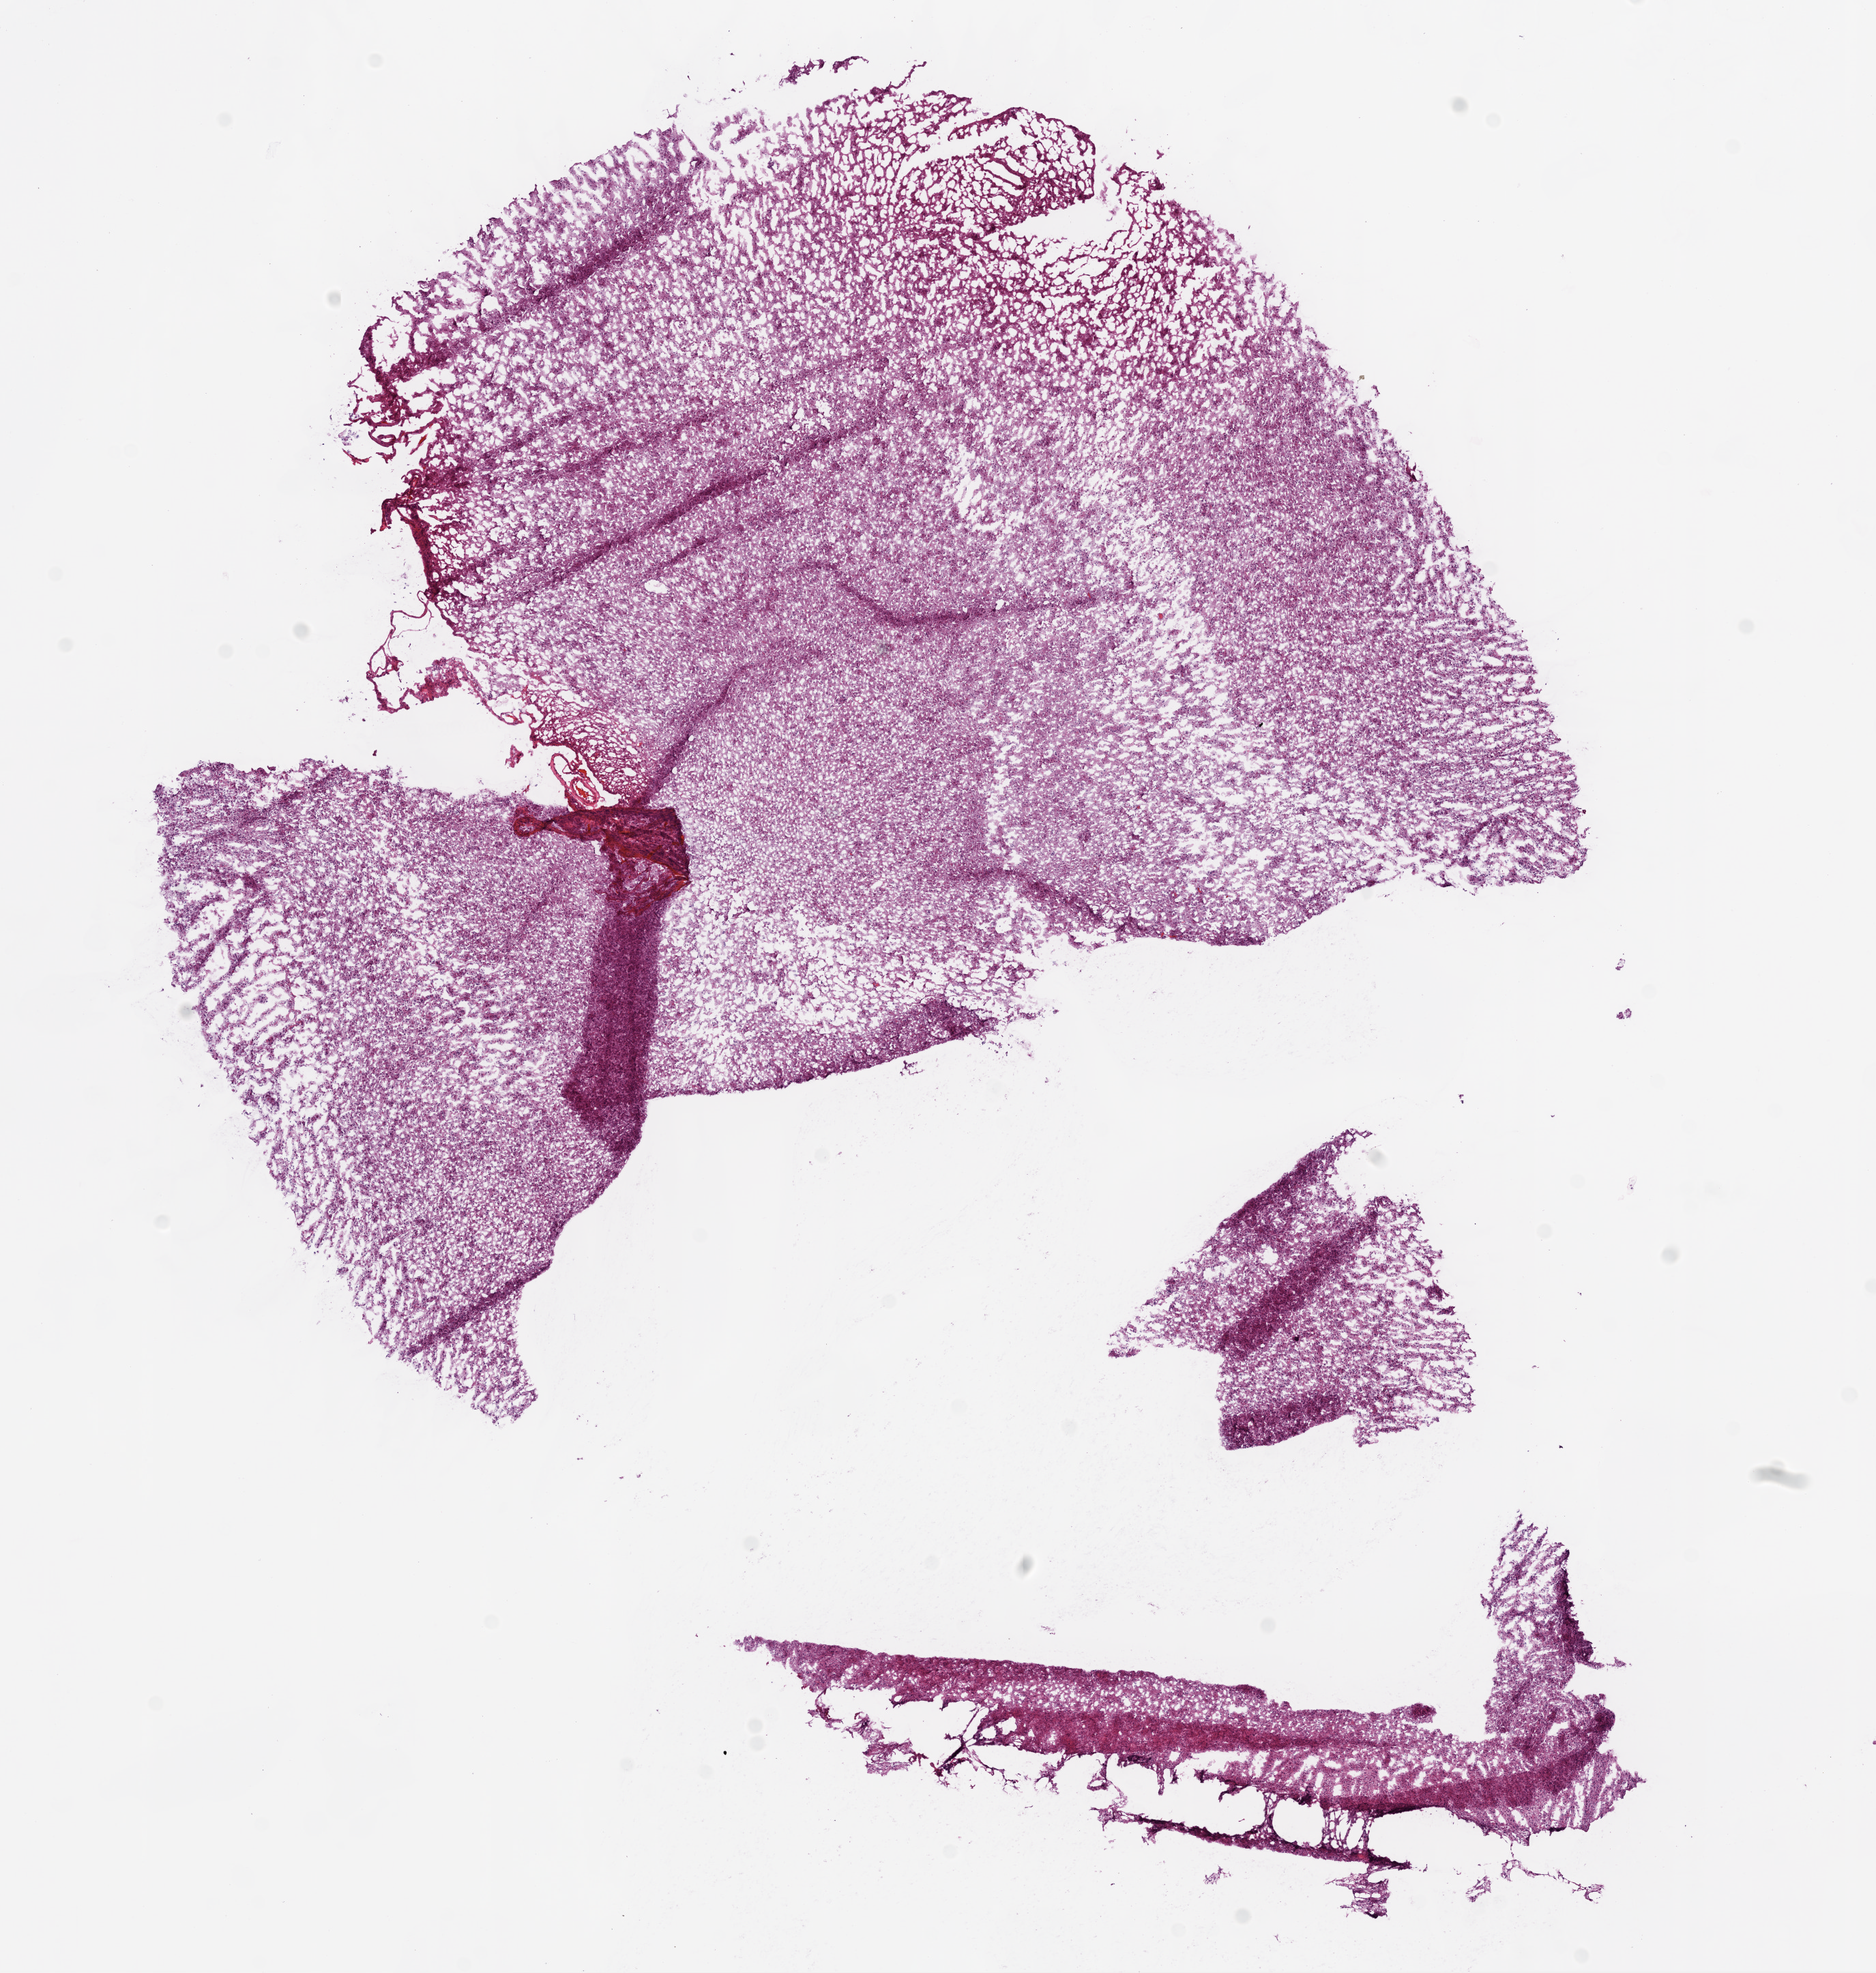
Hematoxylin and eosin (H&E) stained whole-slide image, whole scanned area (about 11.0 x 11.6 mm, from a 20x scan) shown as a low-resolution overview, frozen section from the bottom of the tissue portion, primary tumour sample from the brain. Patient: male, age at initial diagnosis 44 years. Slide review estimates, as recorded: tumour cells 100%, tumour nuclei 80%, normal cells 0%, stromal cells 0%, necrosis 0%.
* pathologic diagnosis: Glioblastoma